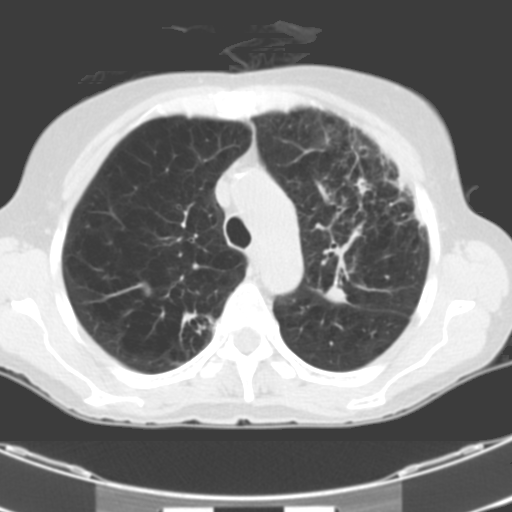
Low-dose screening chest CT, one axial slice. Slice 79 of 106 in the series (ordered by position). One of 2 acquisitions stored at this slice position. Lung window (W 1500 / L -600 HU). 3.2 mm slice thickness. 512 × 512 image matrix.
Annotated regions visible in this slice (expert manual segmentation):
- lesion 1 (tumor): box from (x=324, y=285) to (x=348, y=303) px